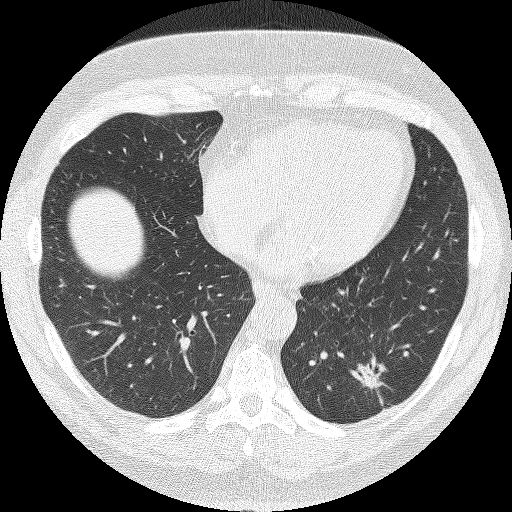
Low-dose screening chest CT, one axial slice. Position 45 of 140 along the scan axis. Lung window (W 1500 / L -600 HU). 512 × 512 image matrix, field of view 349 × 349 mm.
Annotated regions visible in this slice (outlined manually by an expert reader):
- lesion 1 (tumor, lower lobe of left lung): bounding box <351,356,387,393> (left, top, right, bottom; pixels)